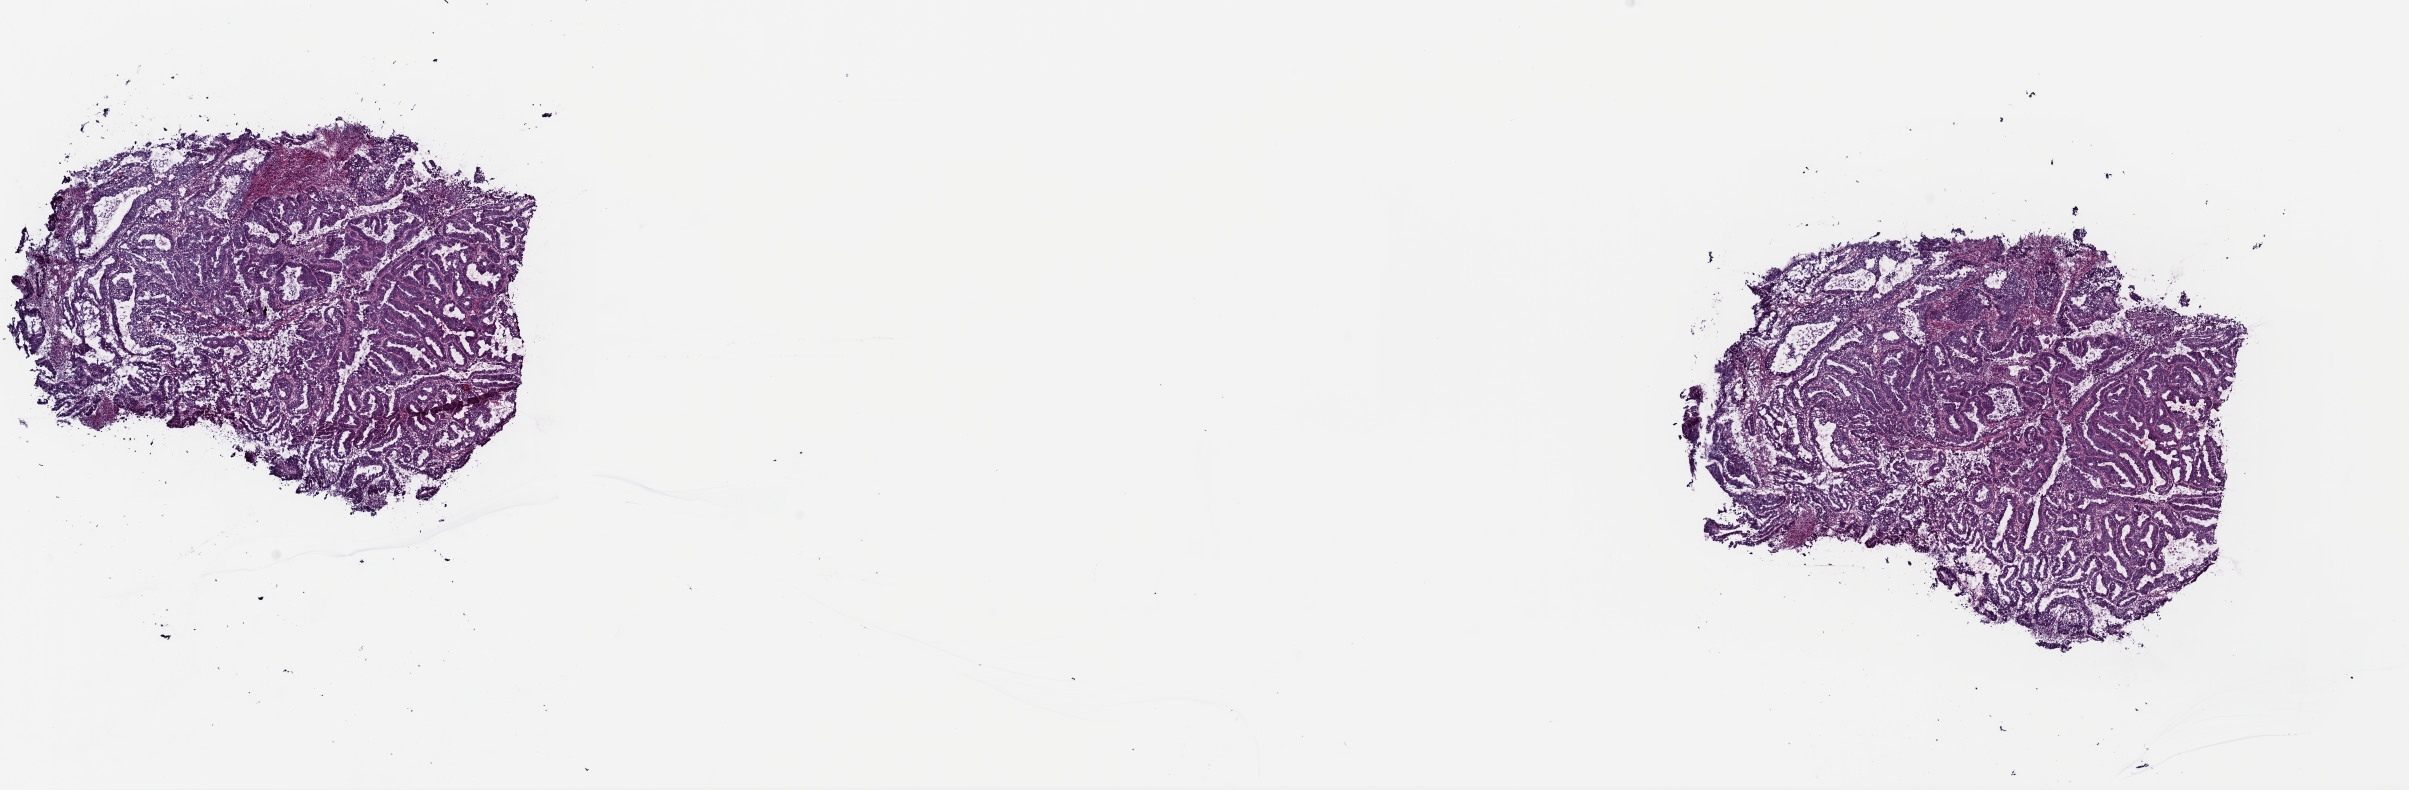
Digitized H&E tissue section (whole slide) — whole scanned area (about 19.0 x 6.2 mm) shown as a low-resolution overview, frozen section from the top of the tissue portion, uterus, primary tumour sample. Patient: female, age at initial diagnosis 70 years. Histologic grade: G3 (poorly differentiated). Pathologist review of this section (percent, as recorded): tumour cells 90%, tumour nuclei 90%, normal cells 0%, stromal cells 5%, necrosis 5%. Infiltration values recorded for this section: lymphocyte infiltration 2%, monocyte infiltration 2%, neutrophil infiltration 1%.
Pathologic diagnosis: Endometrioid adenocarcinoma, NOS (endometrium). FIGO stage: IA.